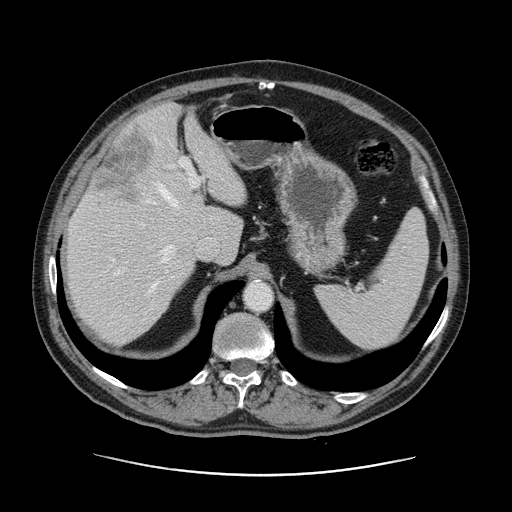
Contrast-enhanced abdominal CT, one axial slice; slice 89 of 141 in the series (ordered by position); intravenous contrast given; soft-tissue window (W 400 / L 40 HU); 2.5 mm slice thickness; 512 × 512 image matrix, field of view 395 × 395 mm. Male patient, age 72 years. From the clinical record (not read from this slice): diagnosis: colorectal cancer liver metastases, imaged before liver resection; multiple liver metastases: yes; largest metastasis: 5.4 cm.
Annotated regions visible in this slice (manually delineated by an expert):
- hepatic veins: bounding box <146,182,177,292> (left, top, right, bottom; pixels)
- liver: <66,104,246,344>
- planned liver remnant (the part of the liver to remain after resection): <66,105,246,344>
- portal vein (with intrahepatic branches): <114,157,202,275>
- liver metastasis: <93,124,151,206>